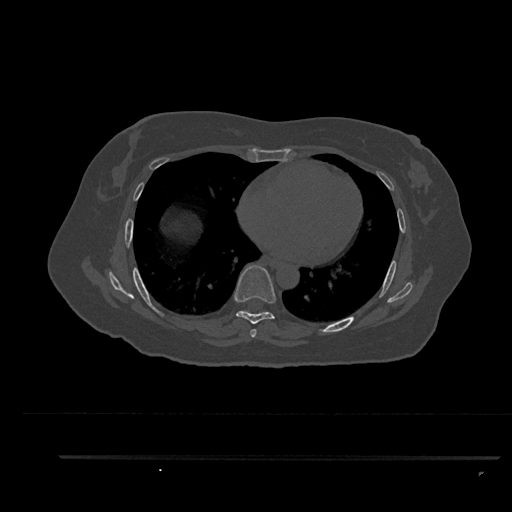
CT including the spine, one axial slice. Slice 504 of 797 in the series (ordered by position). Bone window (W 1800 / L 400 HU). 0.5 mm slice thickness. 512 × 512 image matrix, field of view 408 × 408 mm. Patient: female, 44 years. Case-level facts recorded for this patient, not image findings: primary cancer: renal; vertebrae with lytic lesions (as recorded): L1.
Annotated regions visible in this slice (semi-automatic segmentation, software-assisted and operator-edited):
- T6 vertebra: box from (x=250, y=329) to (x=257, y=338) px
- T7 vertebra: (x=234, y=265)–(x=276, y=336)
- T8 vertebra: (x=247, y=311)–(x=263, y=313)